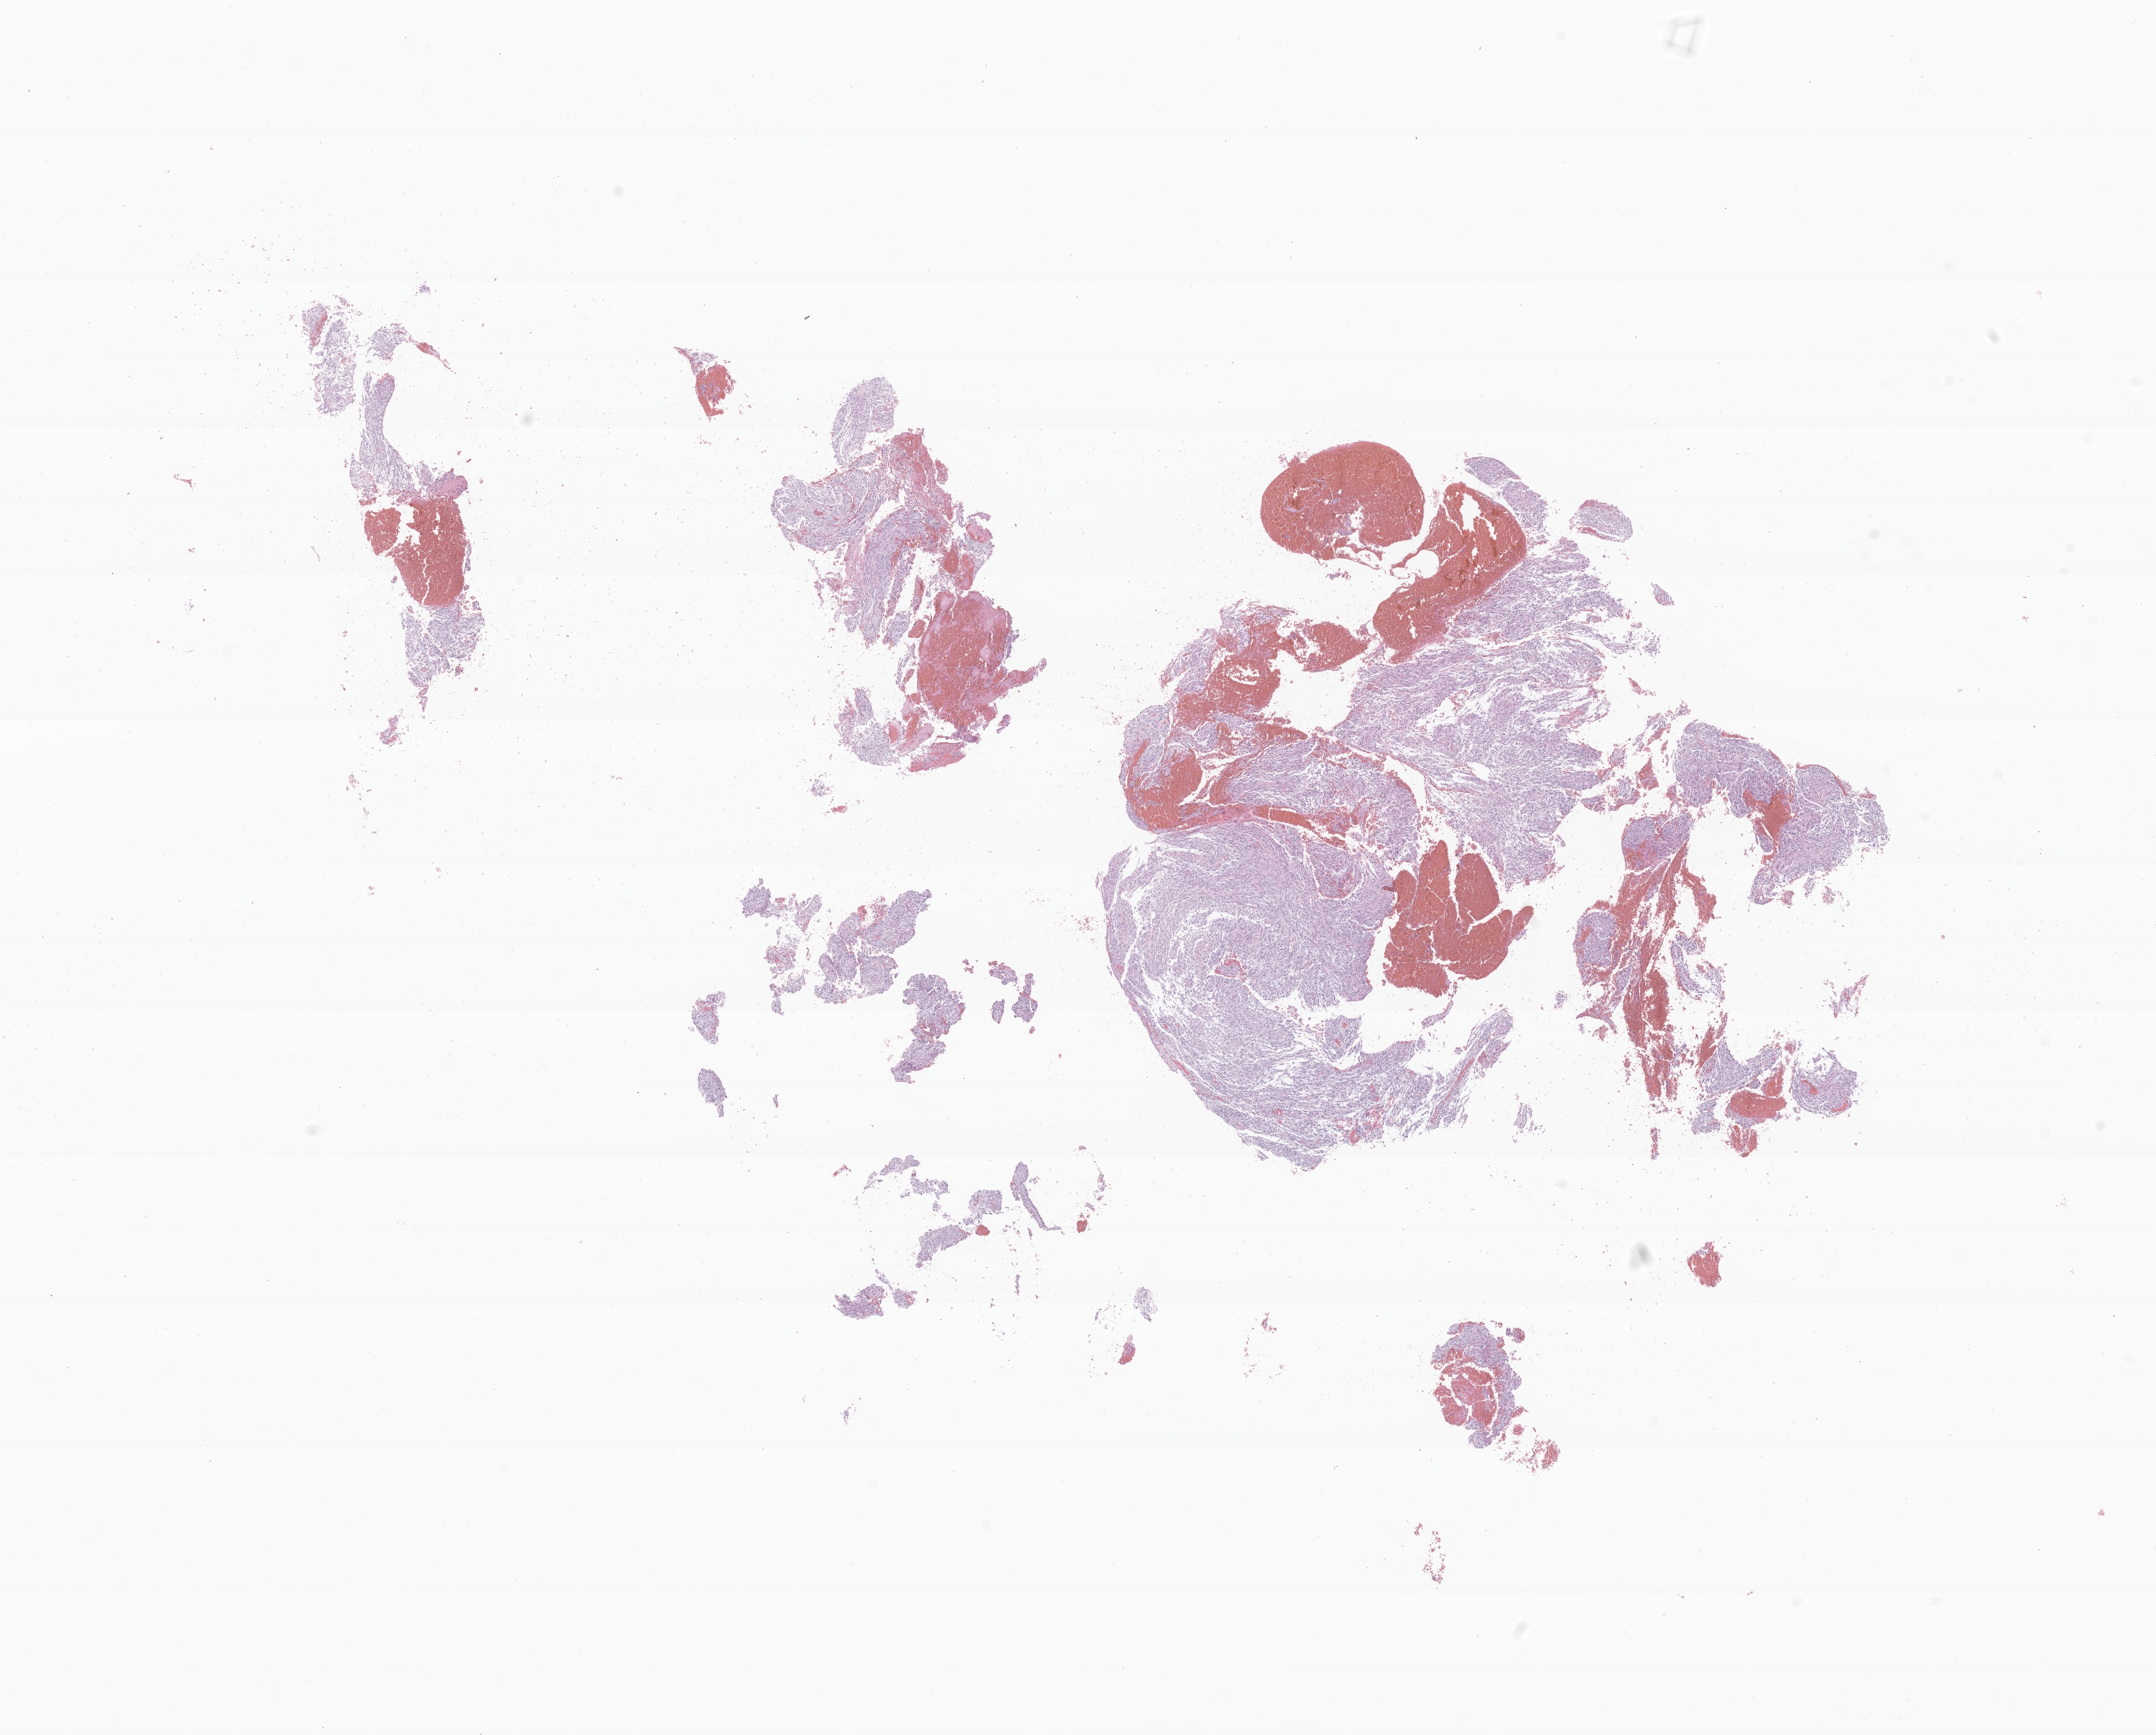
Digitized hematoxylin and eosin (H&E)-stained section of tumor tissue from the brain, shown as a low-resolution overview of the whole scanned area (about 15.7 x 12.7 mm), formalin-fixed paraffin-embedded section. Female patient, age 67 months (5 years 7 months).
• recorded diagnosis: Pilocytic astrocytoma